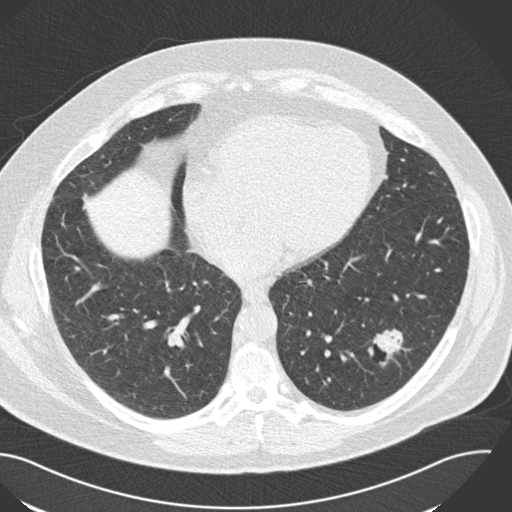
Low-dose screening chest CT, one axial slice; position 69 of 153 along the scan axis; reconstruction kernel B30f; lung window (W 1500 / L -600 HU); 512 × 512 image matrix, field of view 394 × 394 mm.
Structures marked on this image (outlined manually by an expert reader):
- lesion 1 (tumor, lower lobe of left lung): box from (x=373, y=329) to (x=403, y=353) px